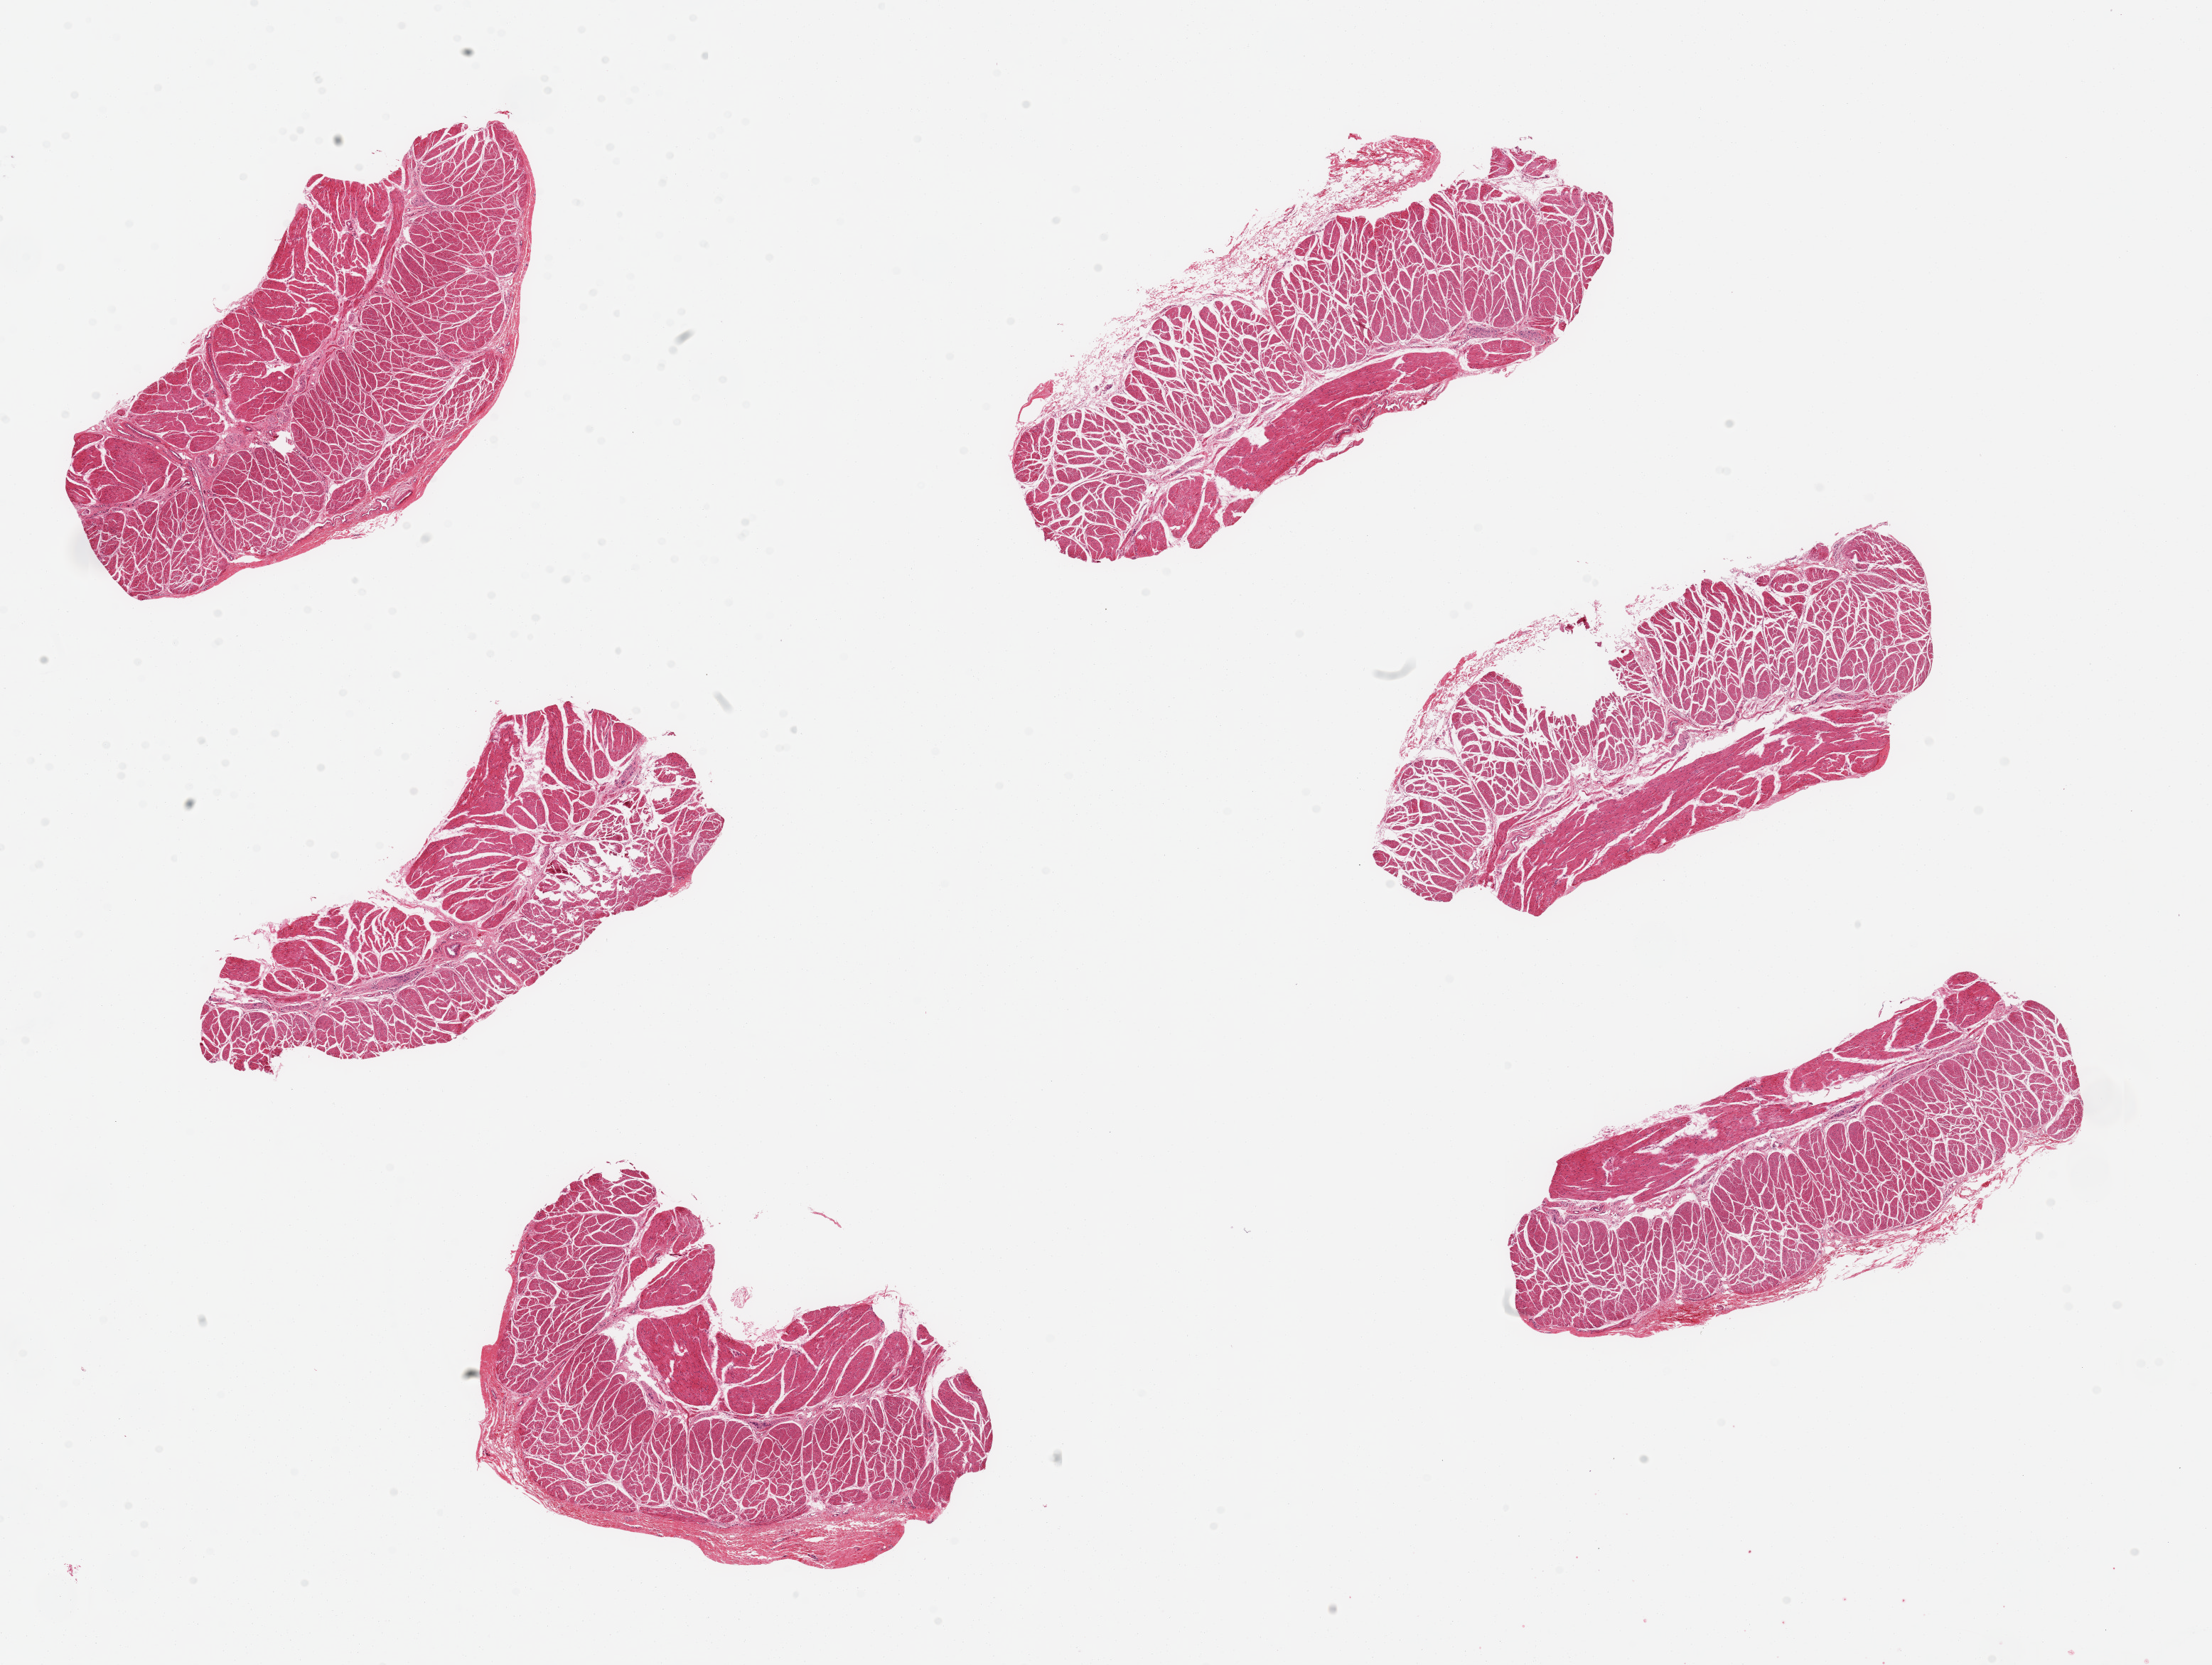
H&E whole-slide image, low-resolution overview of the scanned area, about 24.6 x 18.5 mm (from a 20x scan). PAXgene-fixed, paraffin-embedded tissue. Target tissue: esophageal muscle. Donor tissue sample. Donor sex: female.
- review note (as recorded): 6 pieces, up to 7x3mm